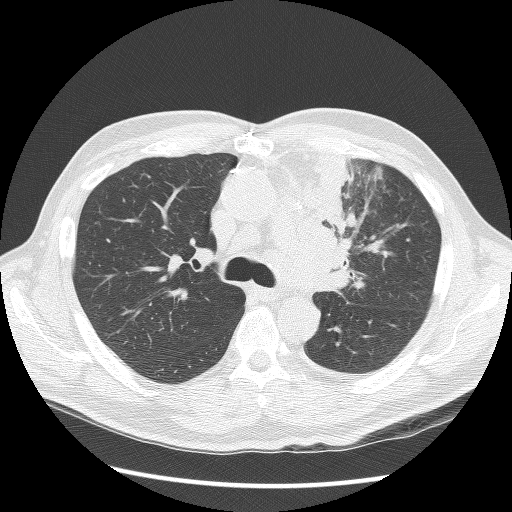
Chest CT (low-dose screening protocol), one axial image, second annual screen, lung window (W 1500 / L -600 HU), lung (sharp) reconstruction kernel (BONE), 120 kVp, slice 45 of 136 in the series. Male participant, aged 64 years at enrolment. Former smoker at enrolment.
Expert reader's lesion annotation, bounding box [x1, y1, x2, y2] px = [300, 157, 376, 287]. Screening reader's record for this exam: no non-calcified nodule ≥4 mm recorded. Participant outcome: lung cancer diagnosed 24 days after this screen — small cell carcinoma, NOS, left upper lobe, stage IV (AJCC 6th edition), 100 mm at pathology.